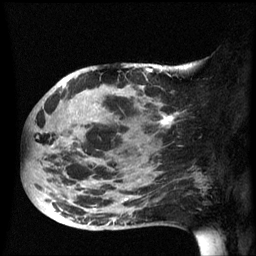
Breast MRI (dynamic contrast-enhanced), one sagittal slice. Position 25 of 60 along the scan axis. Dynamic contrast-enhanced series, image 2 of 3 at this slice position (ordered by acquisition). 1.5 T. TE 4.2 ms, TR 8.4 ms. 256 × 256 image matrix. Patient: female, 49 years.
Structures marked on this image (semi-automatically segmented with operator editing):
- analysis volume of interest (the breast-tissue region the enhancement analysis was run in; not a lesion): bounding box (x1, y1, x2, y2) in pixels: (24, 72, 178, 231)
- tumour enhancement mask (voxels above the 70 % enhancement threshold inside the analysis volume of interest): (57, 86, 174, 223)